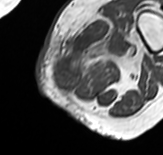
MRI of an extremity soft-tissue mass, one axial slice. Slice 14 of 65 in the series (ordered by position). MR volume resampled by the dataset authors to the PET/CT grid (not the native acquisition matrix). 3.27 mm slice thickness. 163 × 155 image matrix, field of view 159 × 151 mm. Female patient. From the clinical record (not read from this slice): histological type: pleomorphic leiomyosarcoma; grade: high; site of the primary tumour: left thigh.
Structures marked on this image (expert contour drawn on MRI and transferred to this co-registered scan by the dataset authors):
- gross tumour volume including surrounding oedema: bounding box (x1, y1, x2, y2) in pixels: (53, 22, 141, 91)
- gross tumour volume (mass): (55, 67, 81, 89)